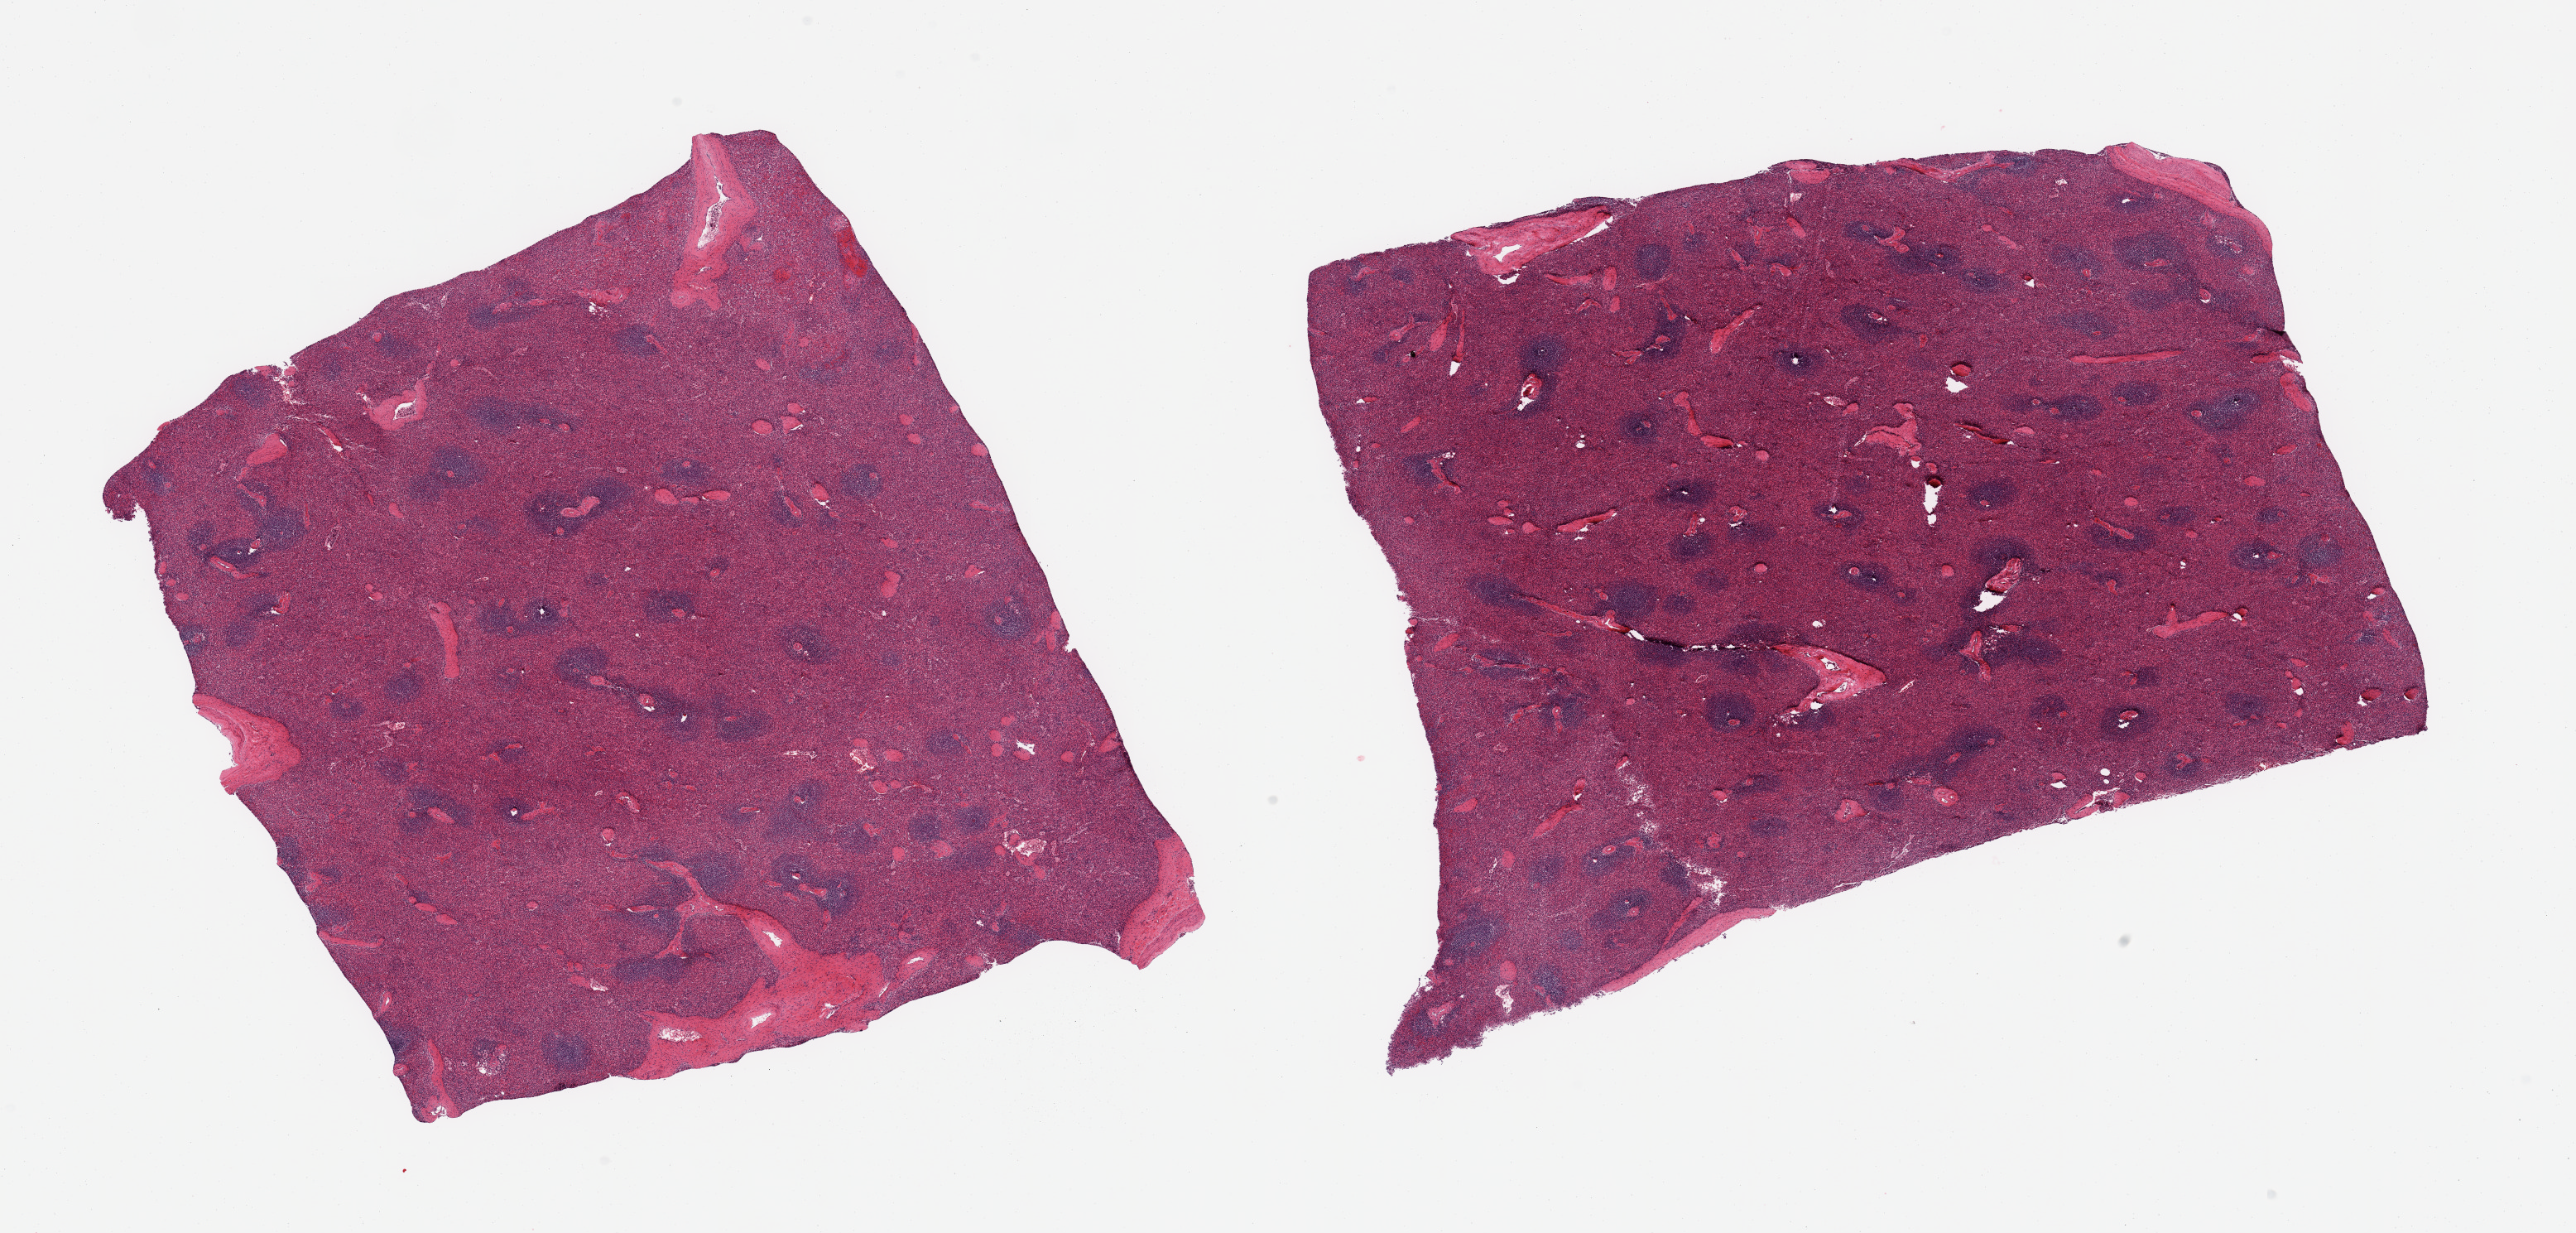
Whole-slide image, haematoxylin and eosin stain — a low-resolution overview of the entire scanned area, about 24.6 x 11.8 mm (from a 20x scan). PAXgene-fixed paraffin-embedded (PFPE) section. Section of spleen (target tissue). Tissue donor sample. Male donor.
* pathologist's review note for this sample: 2 pieces; well lymphoid tissue